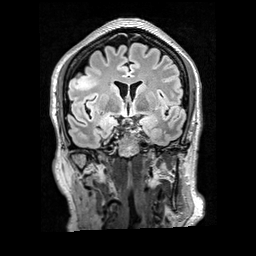
Brain MRI from a brain-tumour surgery series, one coronal slice; position 113 of 200 along the scan axis; T2 FLAIR; 256 × 256 image matrix, field of view 256 × 256 mm. Case-level facts recorded for this patient, not image findings: histopathology: Glioblastoma; WHO grade: 4; IDH mutation: no; tumour location: Right Frontal.
Structures marked on this image (outlined manually by an expert reader):
- tumour: bounding box [x1, y1, x2, y2] px = [72, 71, 101, 91]